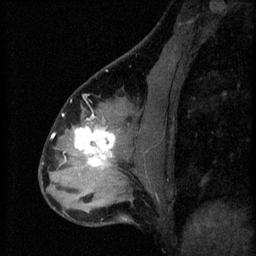
Breast MRI (dynamic contrast-enhanced), one sagittal slice. Position 24 of 60 along the scan axis. 3 images stored at this slice position (order not interpretable as contrast timing). 1.5 T. TE 4.2 ms, TR 8.2 ms. 2.3 mm slice thickness. 256 × 256 image matrix, field of view 180 × 180 mm. Female patient, age 37 years.
Outlined on this slice (semi-automatically segmented with operator editing):
- analysis volume of interest (the breast-tissue region the enhancement analysis was run in; not a lesion): bounding box [x1, y1, x2, y2] px = [67, 120, 122, 179]
- tumour enhancement mask (voxels above the 70 % enhancement threshold inside the analysis volume of interest): [74, 120, 115, 167]